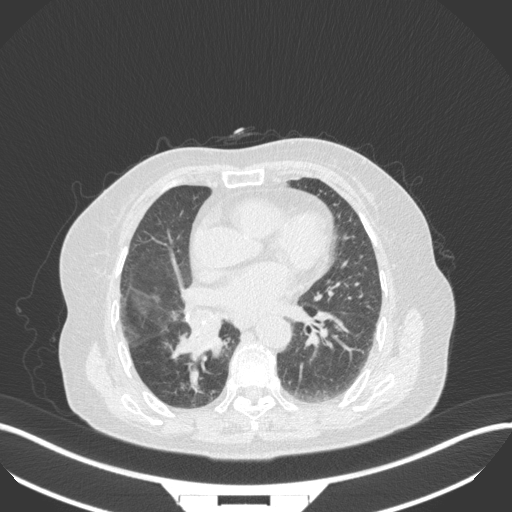
Chest CT, one axial slice. Slice 145 of 329 in the series (ordered by position). Reconstruction kernel B31f. 120 kVp. Lung window (W 1500 / L -600 HU). 1 mm slice thickness. 512 × 512 image matrix, field of view 400 × 400 mm. Patient: female, 75 years. From the clinical record (not read from this slice): clinical TNM (as recorded): T1b N0 M1a; histopathological grade: G1.
Structures marked on this image (bounding box drawn by a radiologist):
- lung tumour (recorded histology: squamous cell carcinoma): box from (x=170, y=314) to (x=224, y=361) px